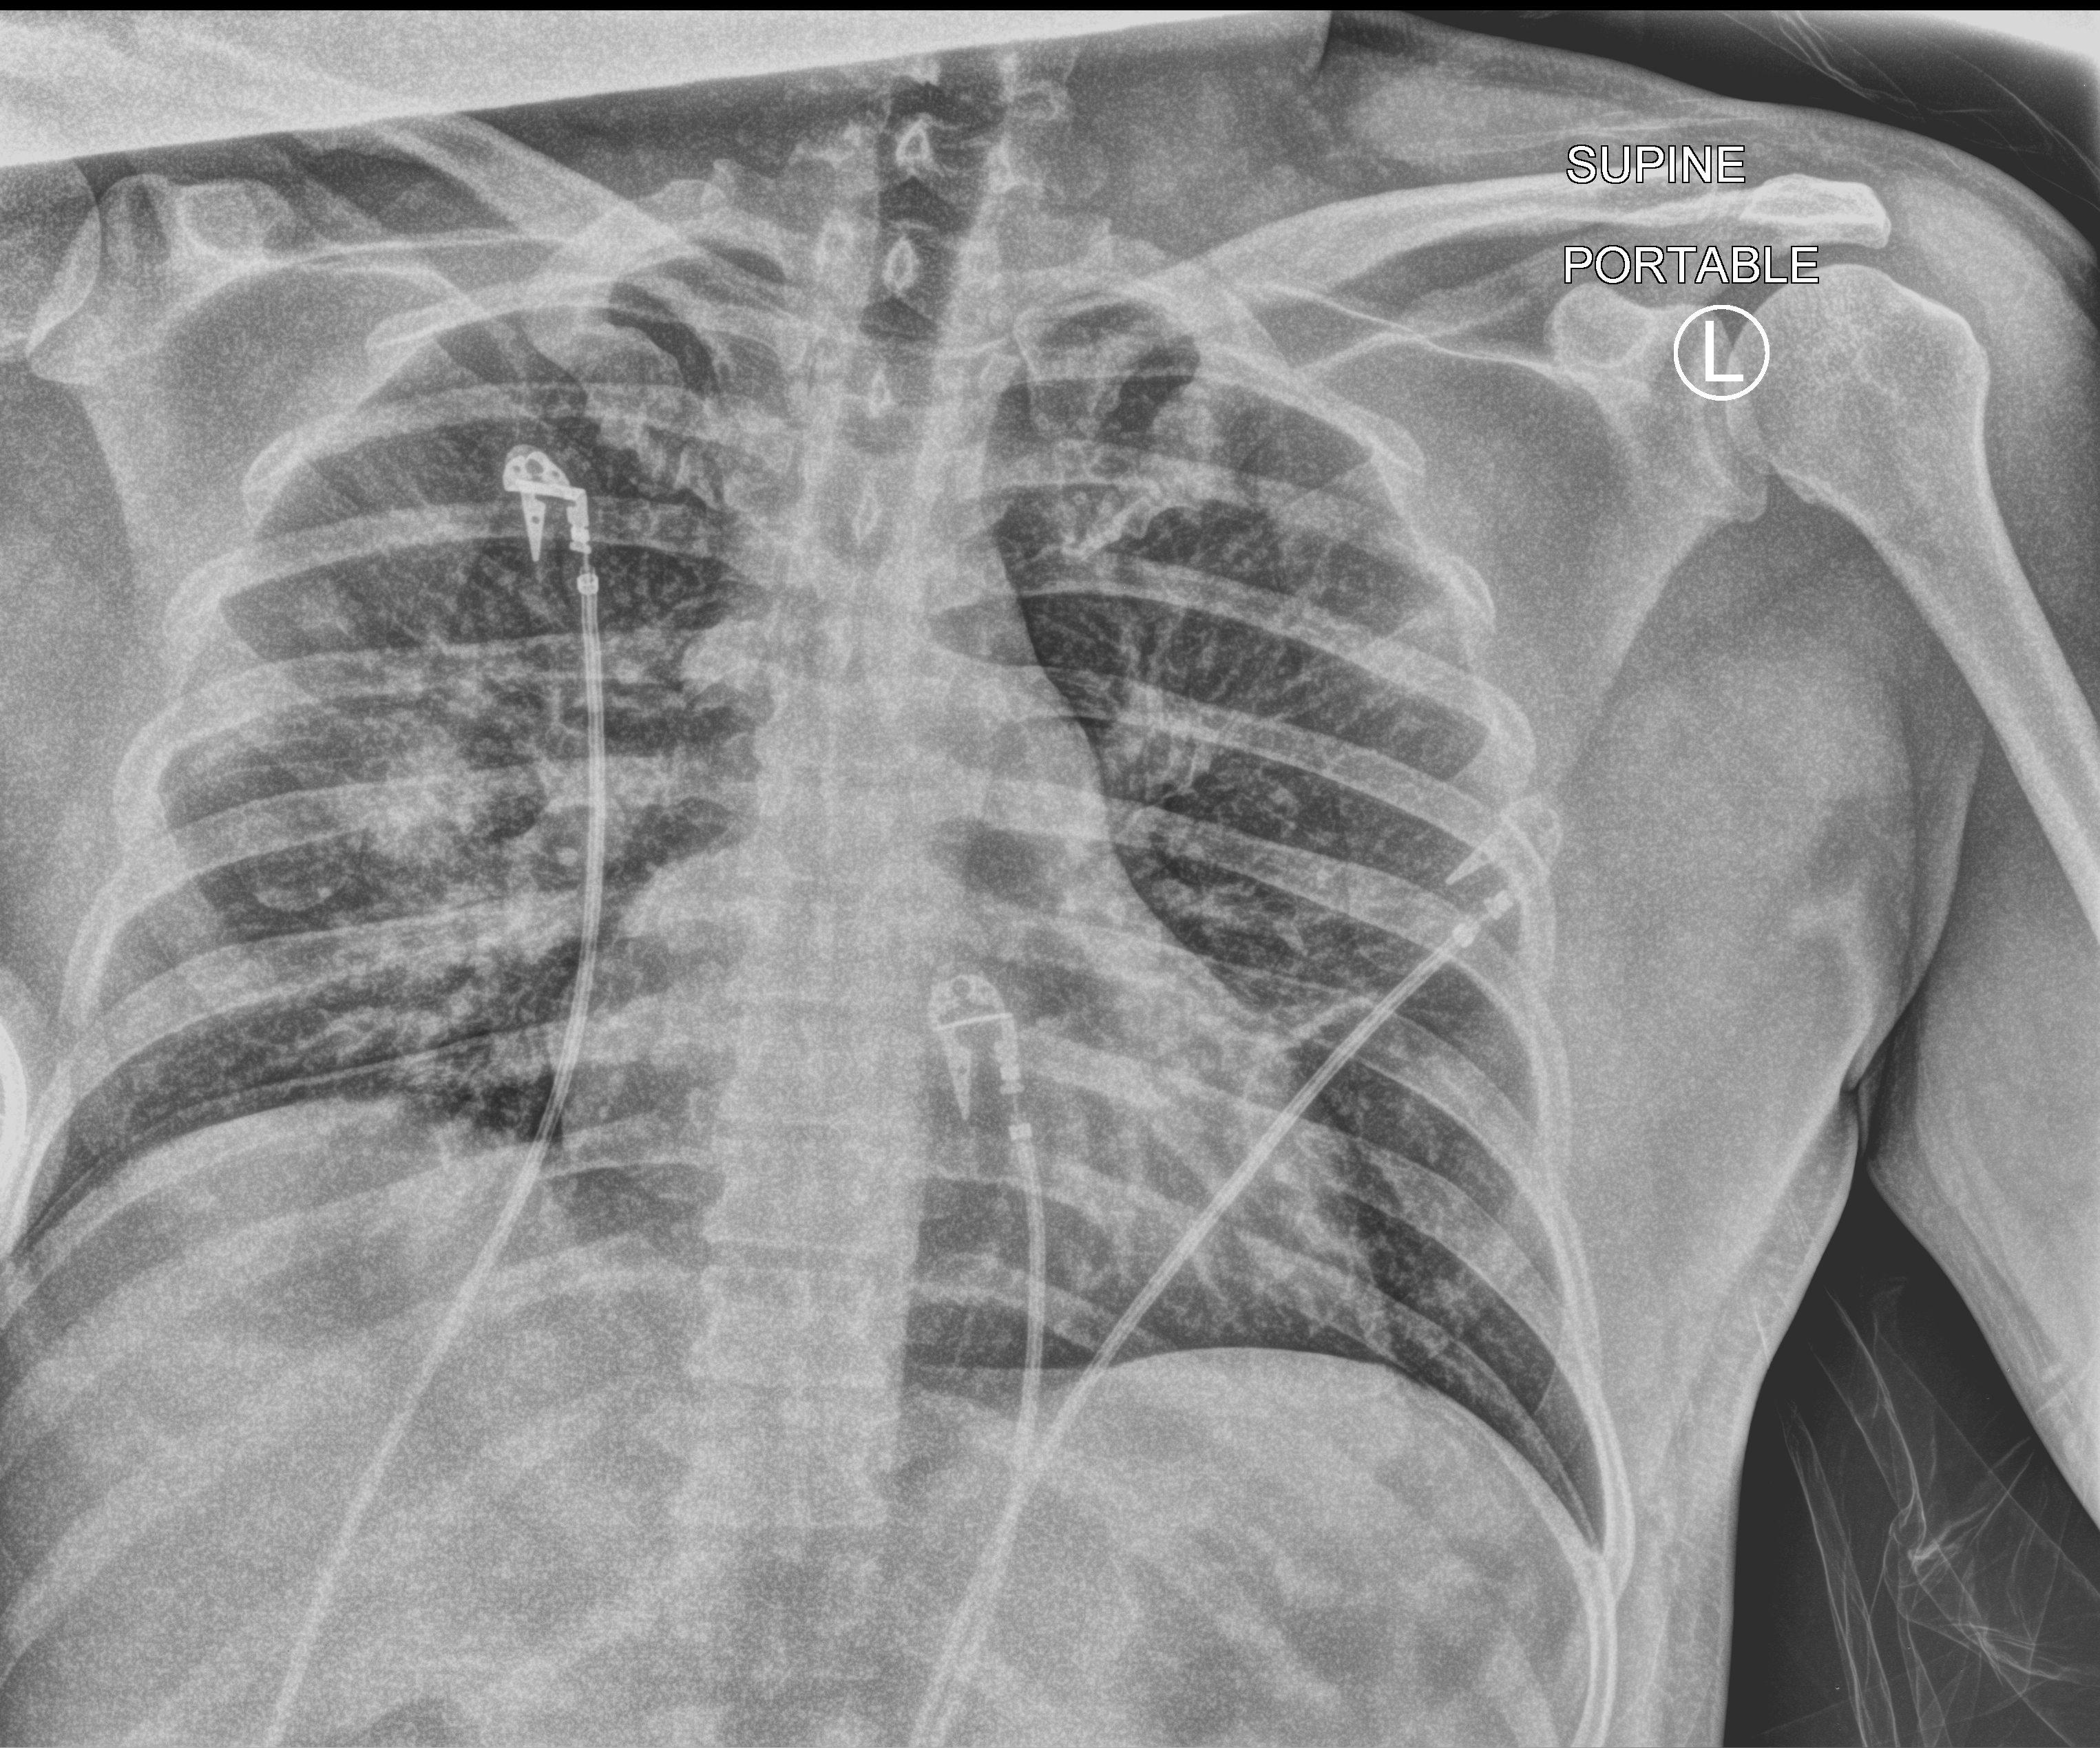
Portable chest radiograph. Male patient hospitalised with COVID-19, age 18–59 years.
From the hospital-stay record, not from the radiograph (when in the stay this image was taken is not recorded): smoking status (admission record): never; admitted to intensive care during this hospital stay: no.